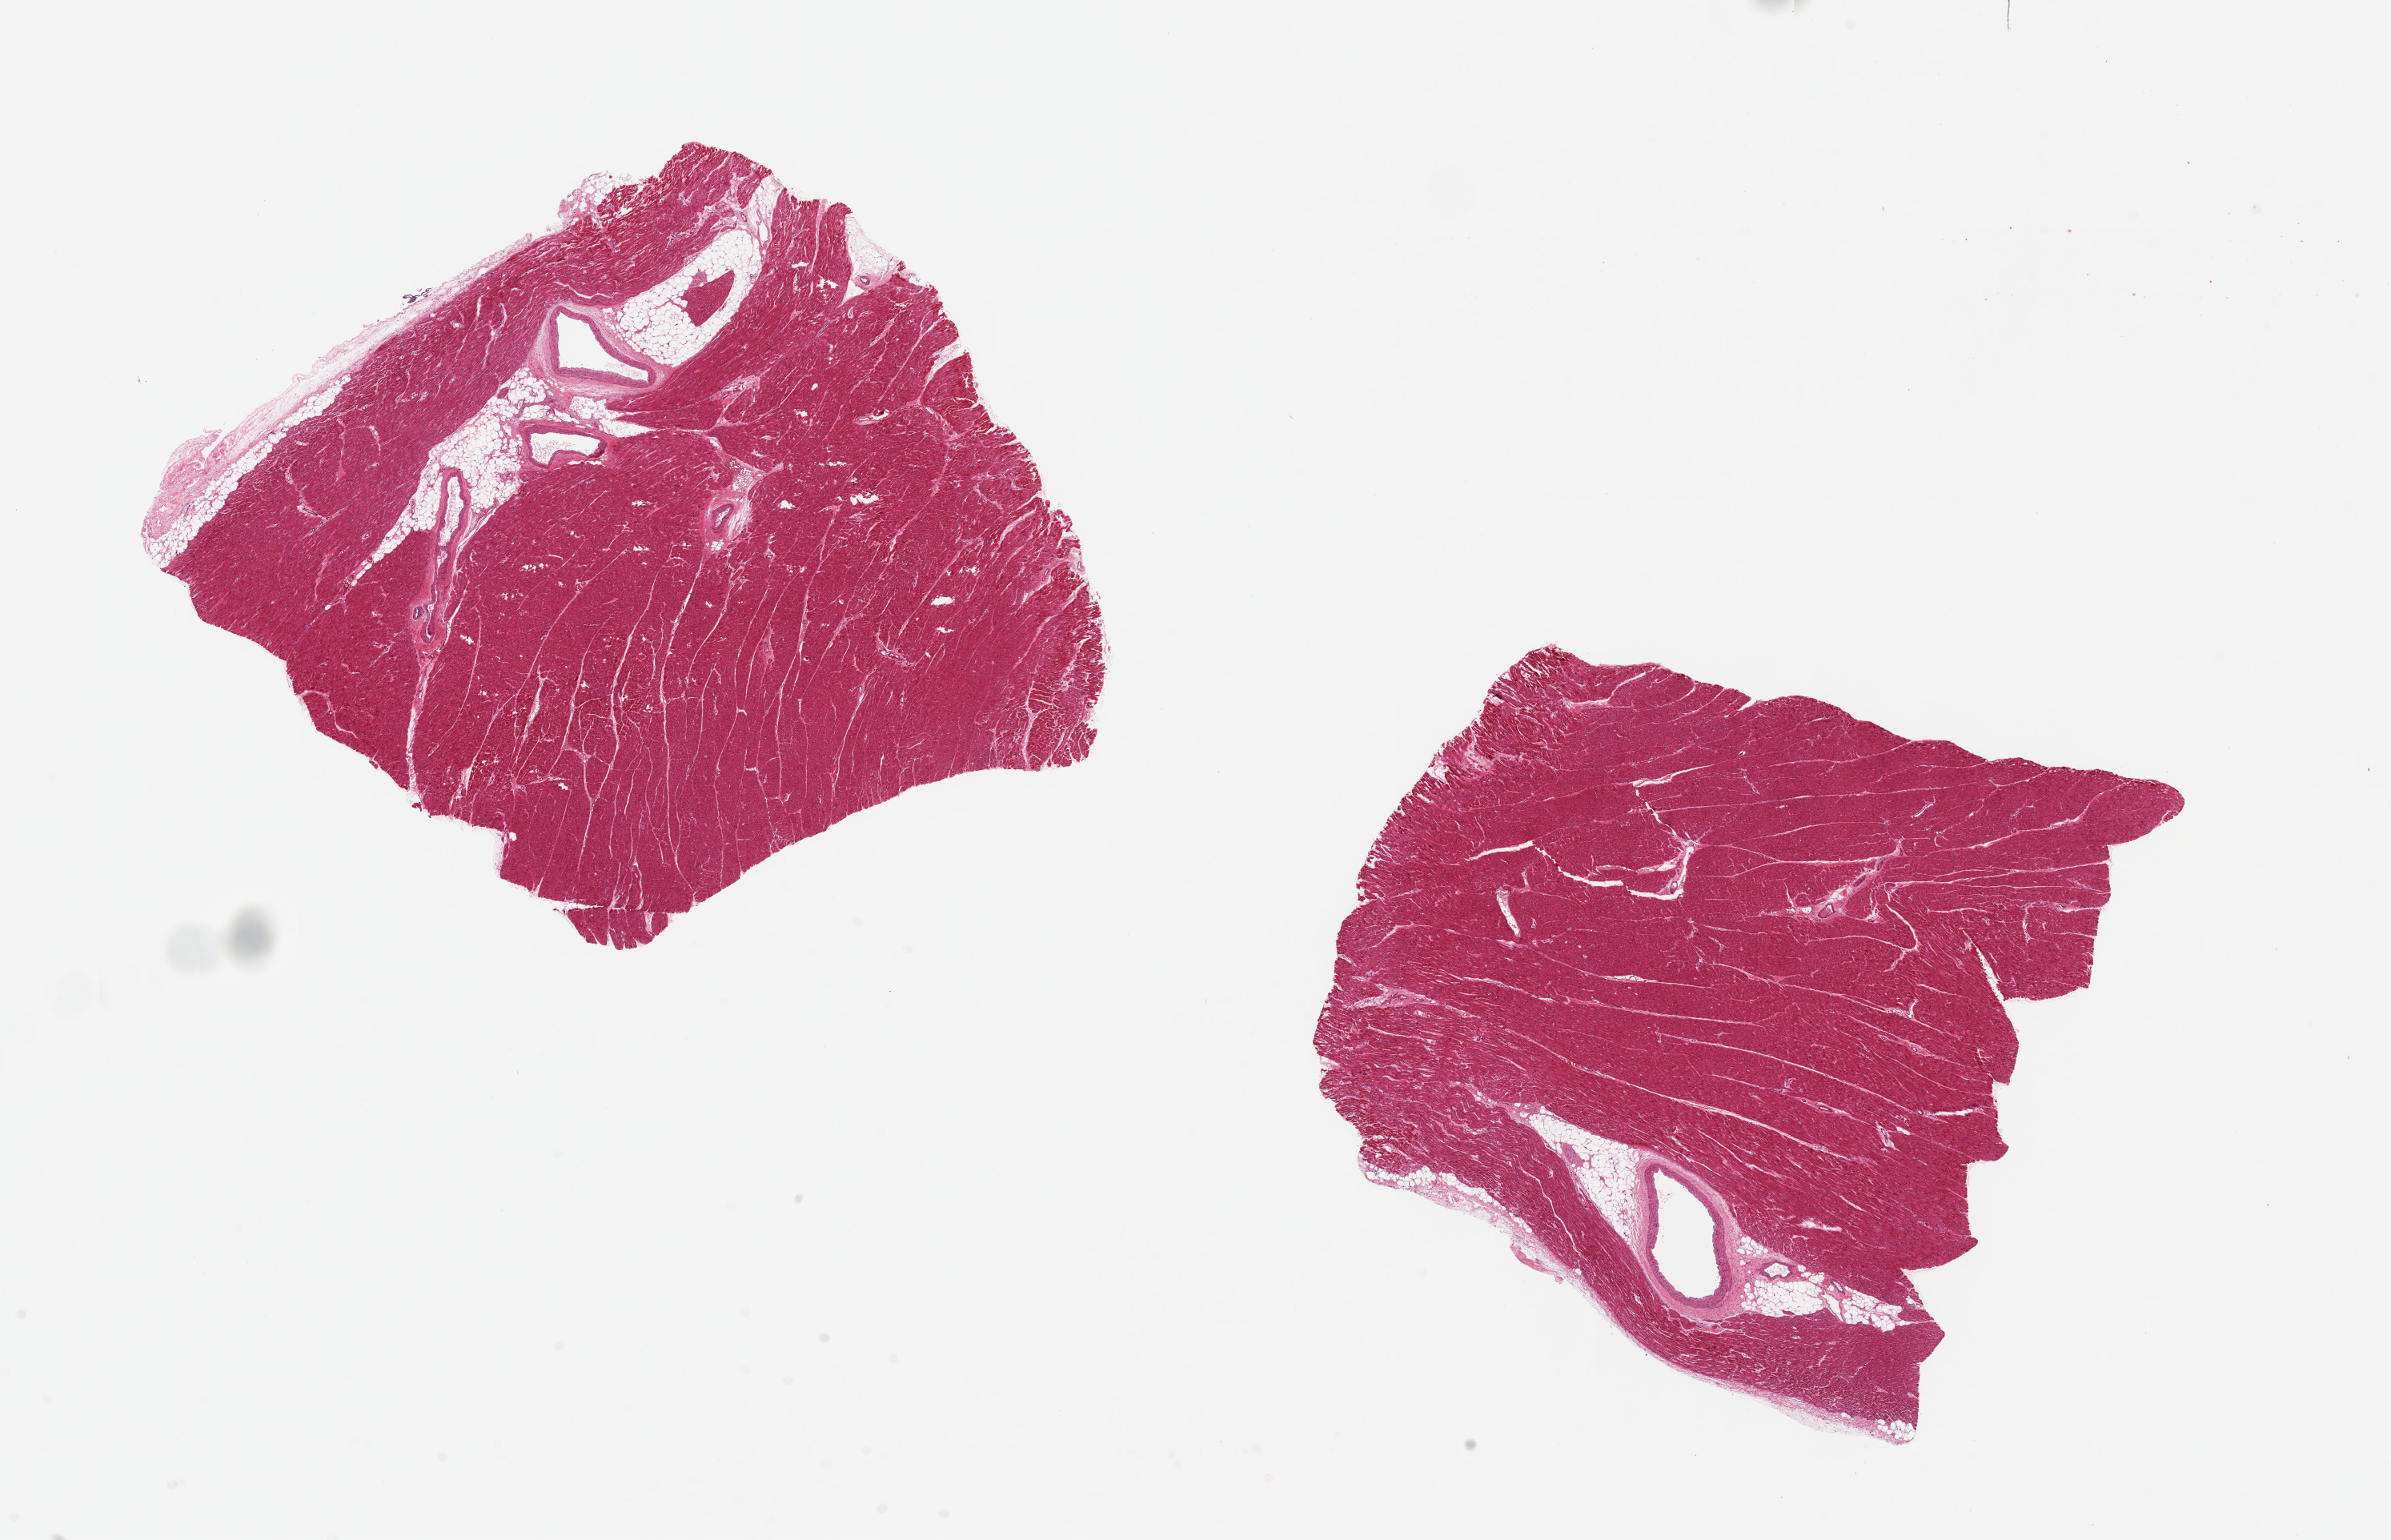
H&E whole-slide image, shown as a low-resolution overview of the whole scanned area (about 23.6 x 15.2 mm, from a 20x scan). PAXgene-fixed, paraffin-embedded tissue. Target tissue: heart. Donor tissue sample. Male donor.
- review note (as recorded): 2 pieces, 7x7 & 7x7mm; ~10% internal adipose around blood vessels; contraction bands